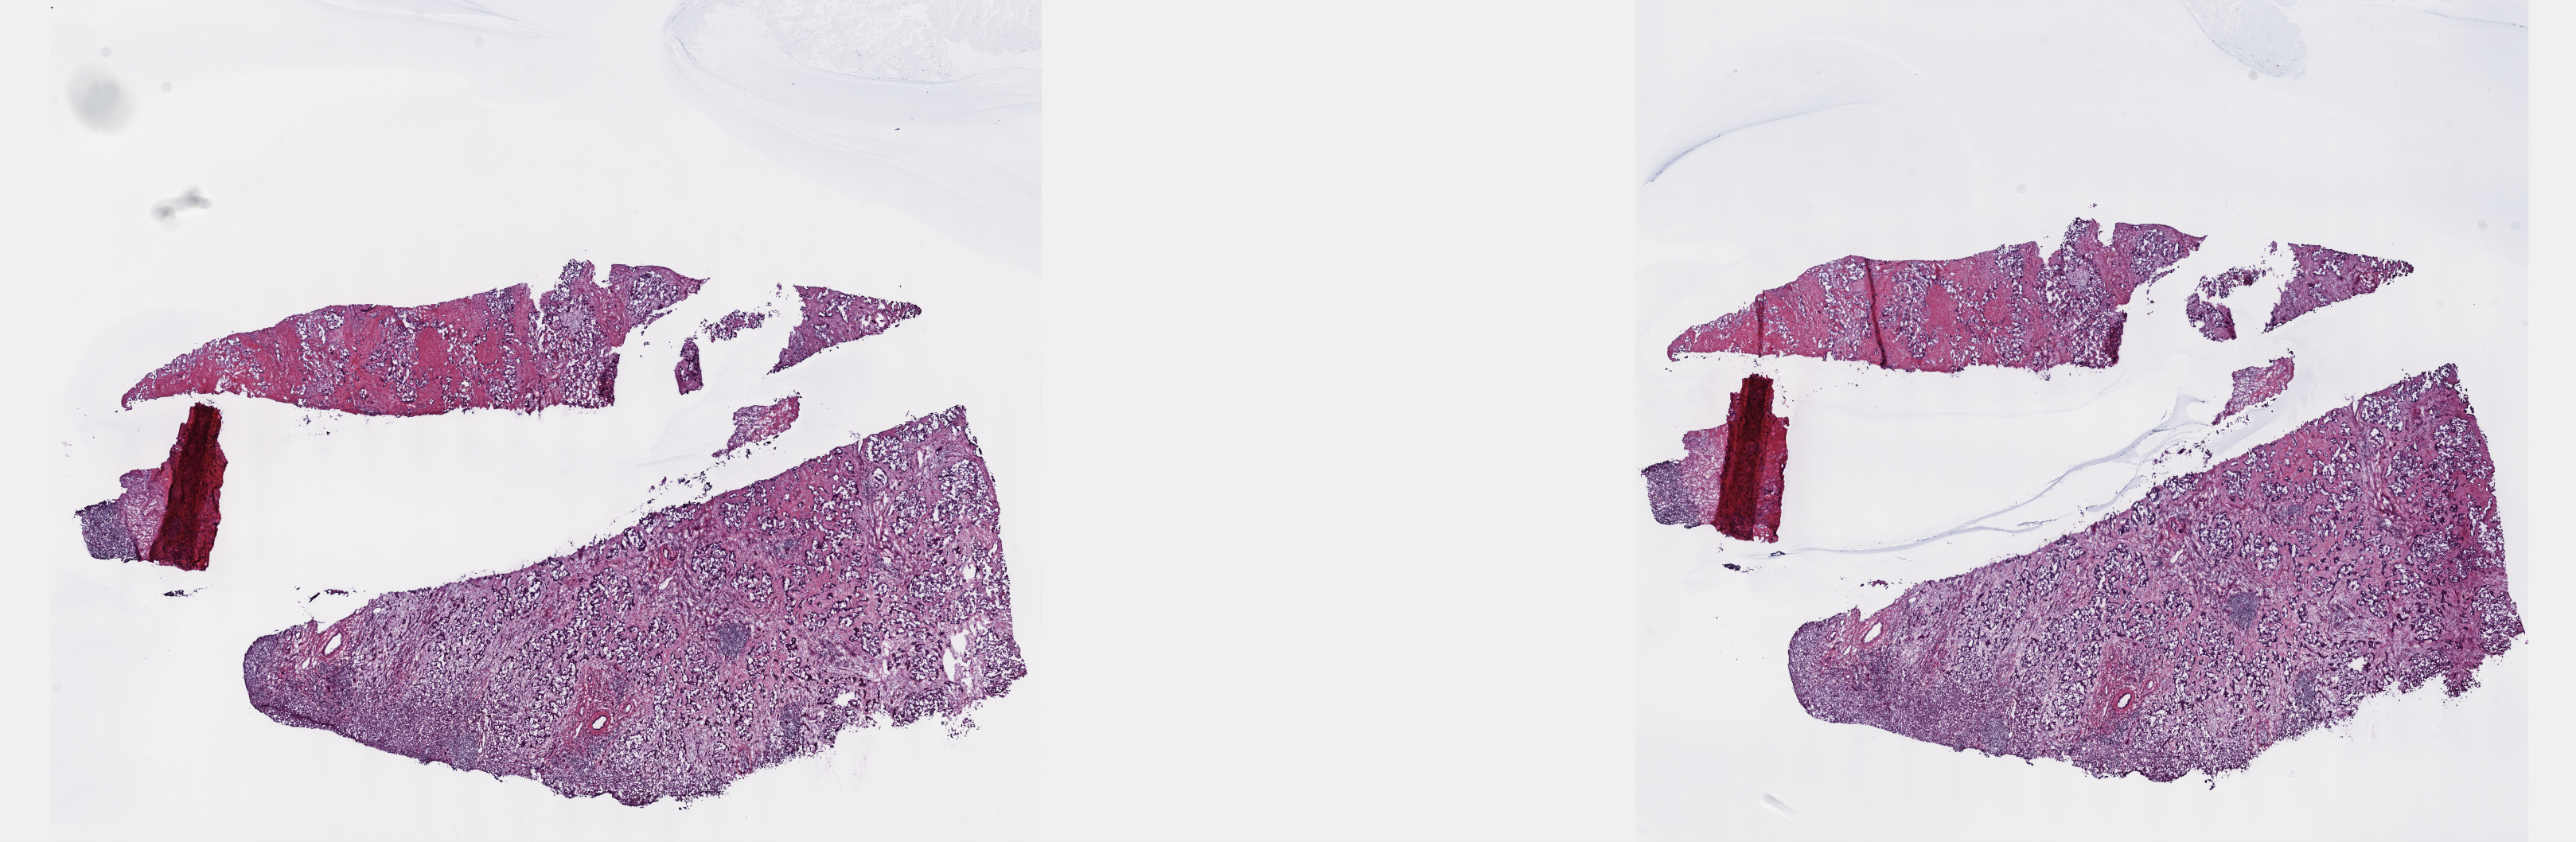
Digitized Hematoxylin and eosin (H&E) stained tissue section (whole slide) — low-resolution overview of the scanned area, about 26.2 x 8.5 mm (from a 40x scan); frozen section from the top of the tissue portion; primary tumour sample from the bile duct. Female patient; age at initial diagnosis 50 years. Histologic grade: G2 (moderately differentiated). Composition of this section per pathologist review: tumour cells 50%, tumour nuclei 60%, normal cells 10%, stromal cells 40%, necrosis 0%. Infiltration values recorded for this section: lymphocyte infiltration 0%, monocyte infiltration 0%, neutrophil infiltration 0%.
Pathologic diagnosis: Cholangiocarcinoma (intrahepatic bile duct). TNM: T2b NX M0. AJCC pathologic stage: II.